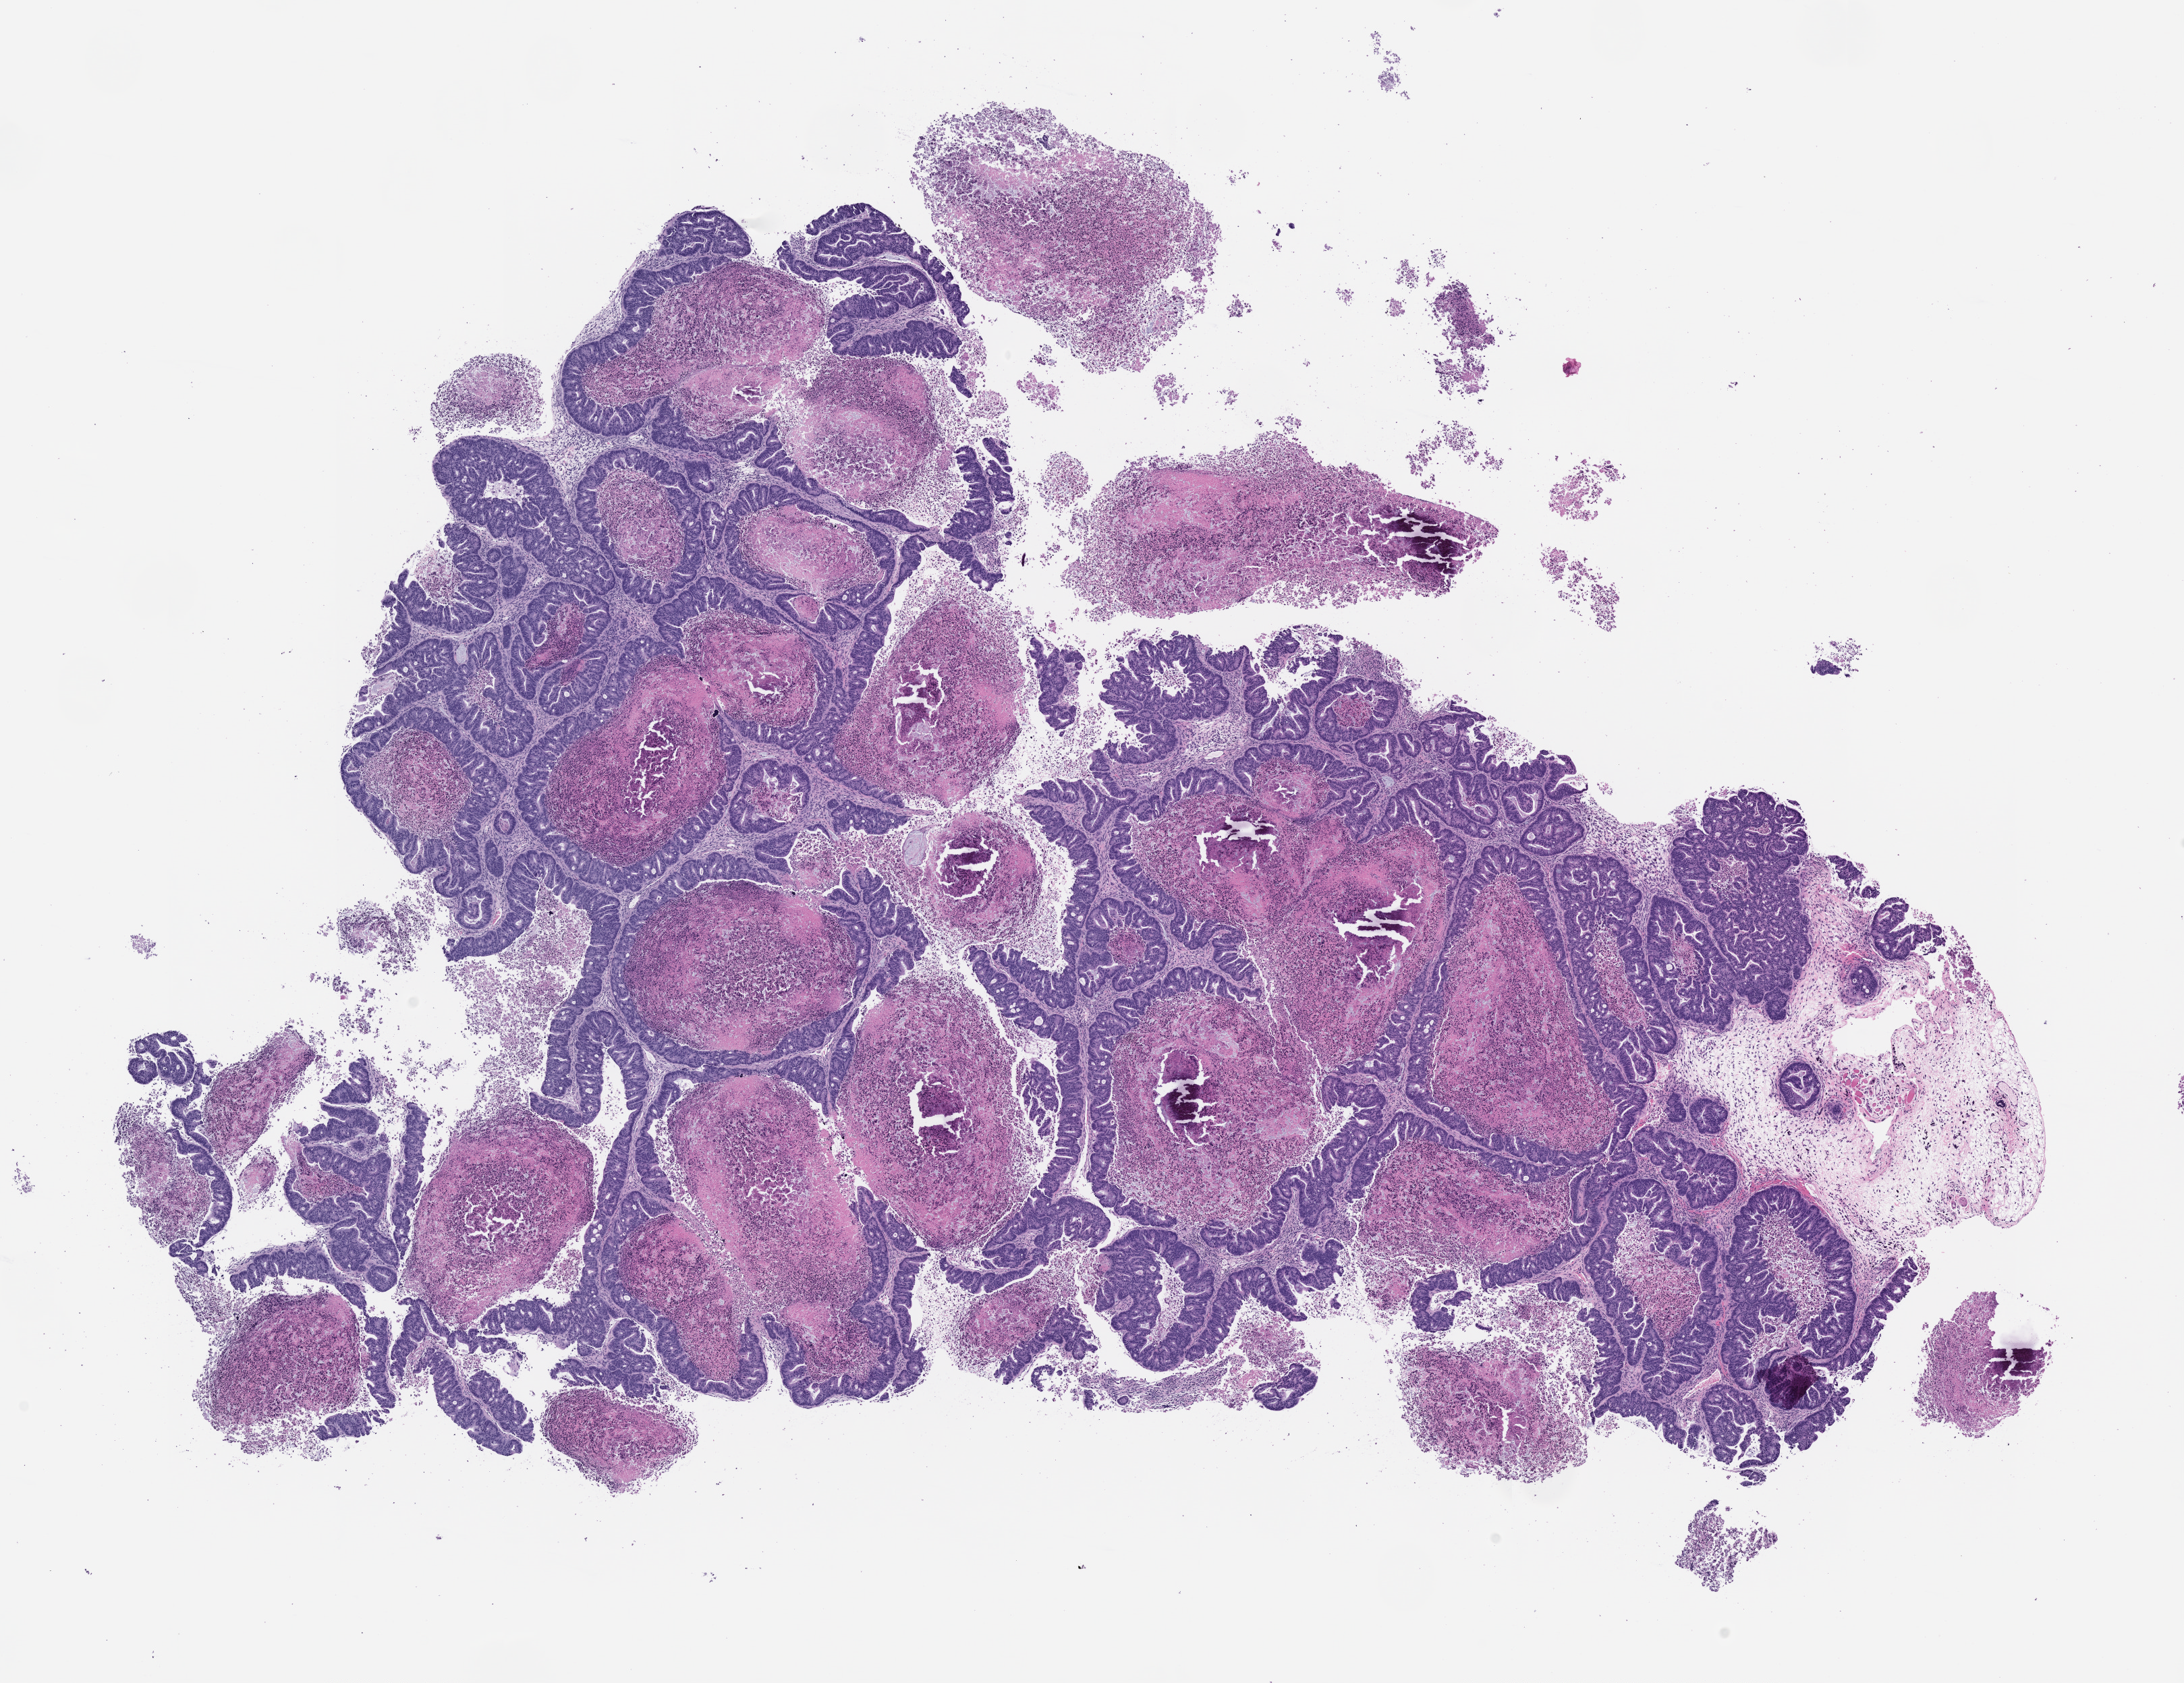
Hematoxylin and eosin (H&E) whole-slide image of a patient-derived xenograft (PDX) tumor grown in a mouse, passage 0 — whole scanned area (about 13.0 x 10.0 mm) shown as a low-resolution overview; formalin-fixed, paraffin-embedded (FFPE) tissue; originating tumor site category: rectum.
- originating patient diagnosis: Rectal Adenocarcinoma